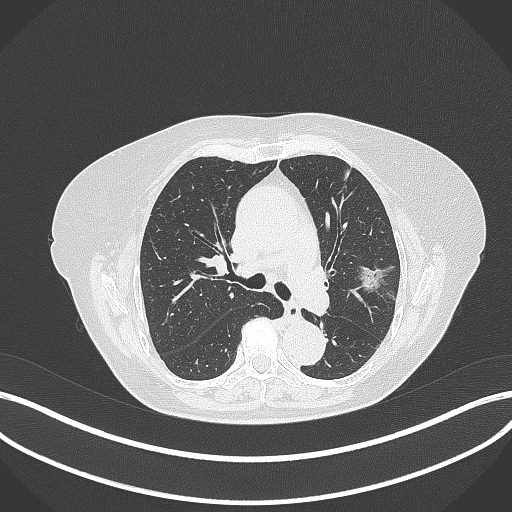
Chest CT, one axial slice. Position 207 of 316 along the scan axis. Reconstruction kernel B70f. 120 kVp. Lung window (W 1500 / L -600 HU). 1 mm slice thickness. 512 × 512 image matrix, field of view 400 × 400 mm. Female patient, age 75 years. From the clinical record (not read from this slice): clinical TNM (as recorded): T1c N0 M0.
Outlined on this slice (rectangle marked by the reading radiologist):
- lung tumour (recorded histology: adenocarcinoma): bounding box (x1, y1, x2, y2) in pixels: (357, 263, 387, 291)